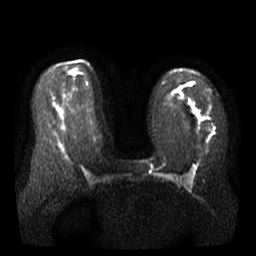
Breast MRI, one axial slice. Position 26 of 41 along the scan axis. Diffusion-weighted series; image 2 of 4 stored at this slice position (different b-values; order by instance number). 3 T. 256 × 256 image matrix, field of view 340 × 340 mm. Female patient.
Structures marked on this image (outlined manually by an expert reader):
- tumour on diffusion-weighted imaging: bounding box <195,109,200,118> (left, top, right, bottom; pixels)